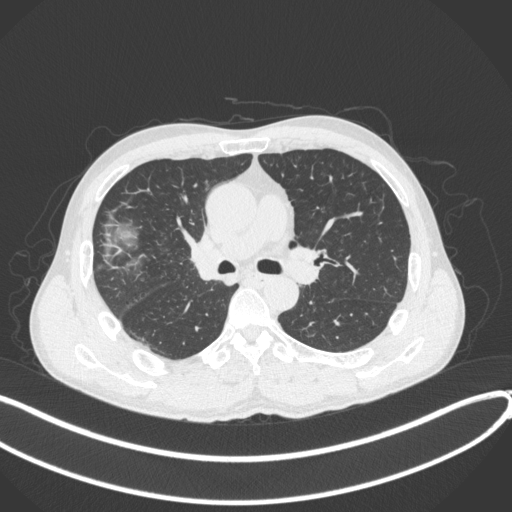
Chest CT, one axial slice. Slice 233 of 409 in the series (ordered by position). 120 kVp. Lung window (W 1500 / L -600 HU). 1 mm slice thickness. 512 × 512 image matrix, field of view 400 × 400 mm. Patient: male, 53 years. Case-level facts recorded for this patient, not image findings: clinical TNM (as recorded): T1b N0 M0.
Structures marked on this image (bounding box drawn by a radiologist):
- lung tumour (recorded histology: squamous cell carcinoma): box from (x=188, y=229) to (x=227, y=290) px